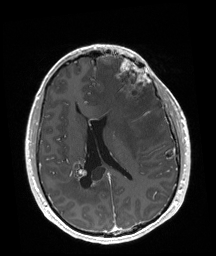
Brain MRI from a brain-tumour surgery series, one axial slice; slice 80 of 192 in the series (ordered by position); T1-weighted post-contrast; 1 mm slice thickness; 216 × 256 image matrix, field of view 219 × 260 mm. Case-level facts recorded for this patient, not image findings: tumour location: Left Frontal.
Outlined on this slice (expert manual segmentation):
- tumour: box from (x=116, y=59) to (x=151, y=103) px